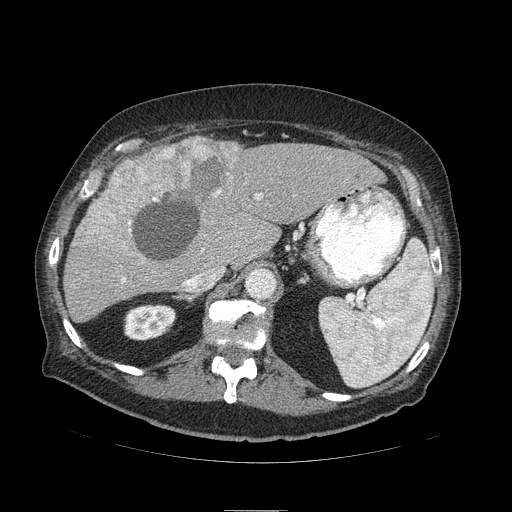
Contrast-enhanced abdominal CT (liver protocol), one axial slice; slice 61 of 103 in the series (ordered by position); reconstruction kernel STANDARD; 120 kVp; soft-tissue window (W 400 / L 40 HU); 2.5 mm slice thickness; 512 × 512 image matrix. Case-level facts recorded for this patient, not image findings: diagnosis: hepatocellular carcinoma (patient treated with transarterial chemoembolisation; whether this scan precedes or follows treatment is not stated here); TNM stage (as recorded): Stage-IIIA; Child-Pugh class: B; tumour differentiation: well differentiated; tumour size: 13 cm.
Outlined on this slice (semi-automatic segmentation, software-assisted and operator-edited):
- liver parenchyma outside the tumour (the mass and vessels are separate outlines, so this box may not span the whole liver): bounding box [x1, y1, x2, y2] px = [64, 142, 384, 322]
- mass: [77, 136, 244, 250]
- liver vessels: [122, 194, 260, 283]